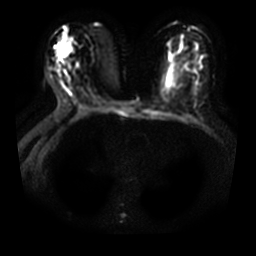
Breast MRI, one axial slice; position 18 of 33 along the scan axis; diffusion-weighted series; image 2 of 4 stored at this slice position (different b-values; order by instance number); 3 T; 256 × 256 image matrix, field of view 350 × 350 mm. Female patient.
Outlined on this slice (outlined manually by an expert reader):
- tumour on diffusion-weighted imaging: bounding box (x1, y1, x2, y2) in pixels: (58, 48, 63, 59)